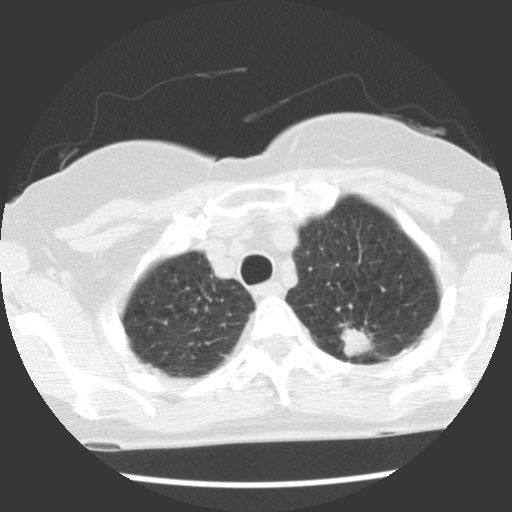
Low-dose screening chest CT, one axial slice. Position 98 of 120 along the scan axis. Reconstruction kernel STANDARD. 140 kVp. Lung window (W 1500 / L -600 HU). 2.5 mm slice thickness. 512 × 512 image matrix, field of view 300 × 300 mm.
Outlined on this slice (outlined manually by an expert reader):
- lesion 1 (tumor, upper lobe of left lung): bounding box (x1, y1, x2, y2) in pixels: (341, 324, 374, 357)